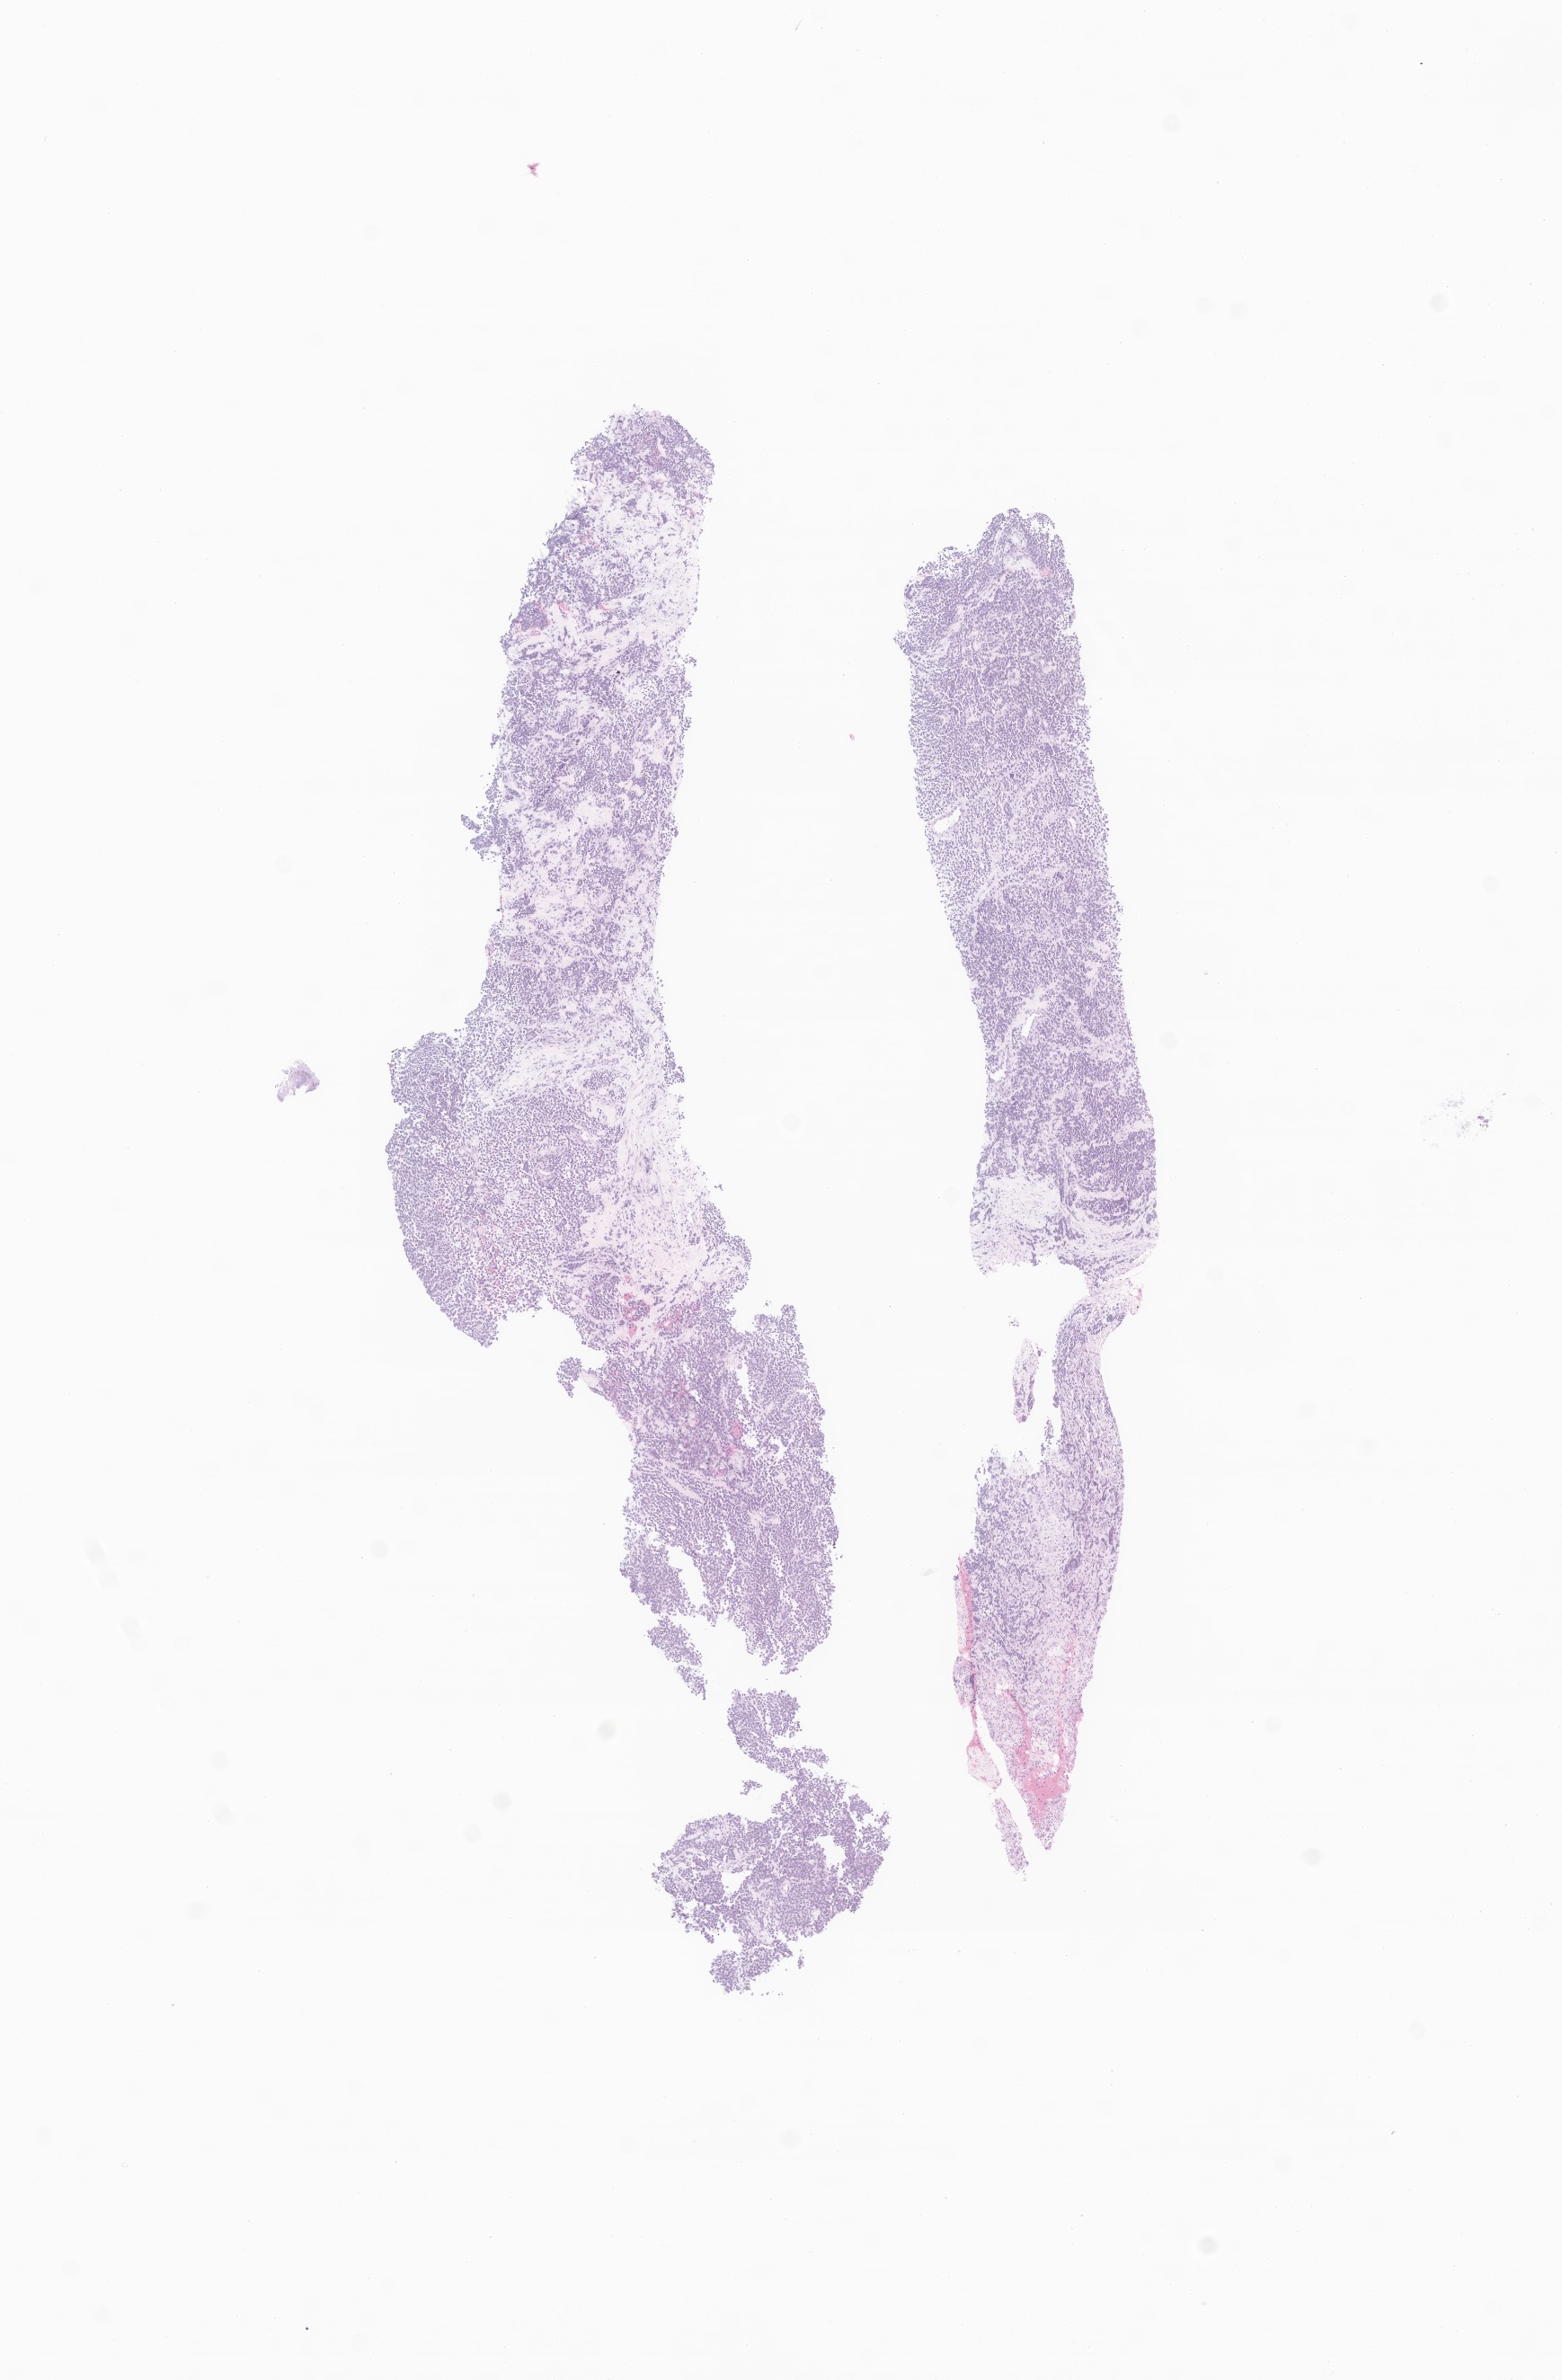
Whole-slide image, H&E stain of tumor tissue from the lymph node — low-resolution overview of the scanned area, about 7.3 x 11.2 mm. Formalin-fixed paraffin-embedded section. Patient: female, age 210 months.
- recorded diagnosis: Alveolar rhabdomyosarcoma